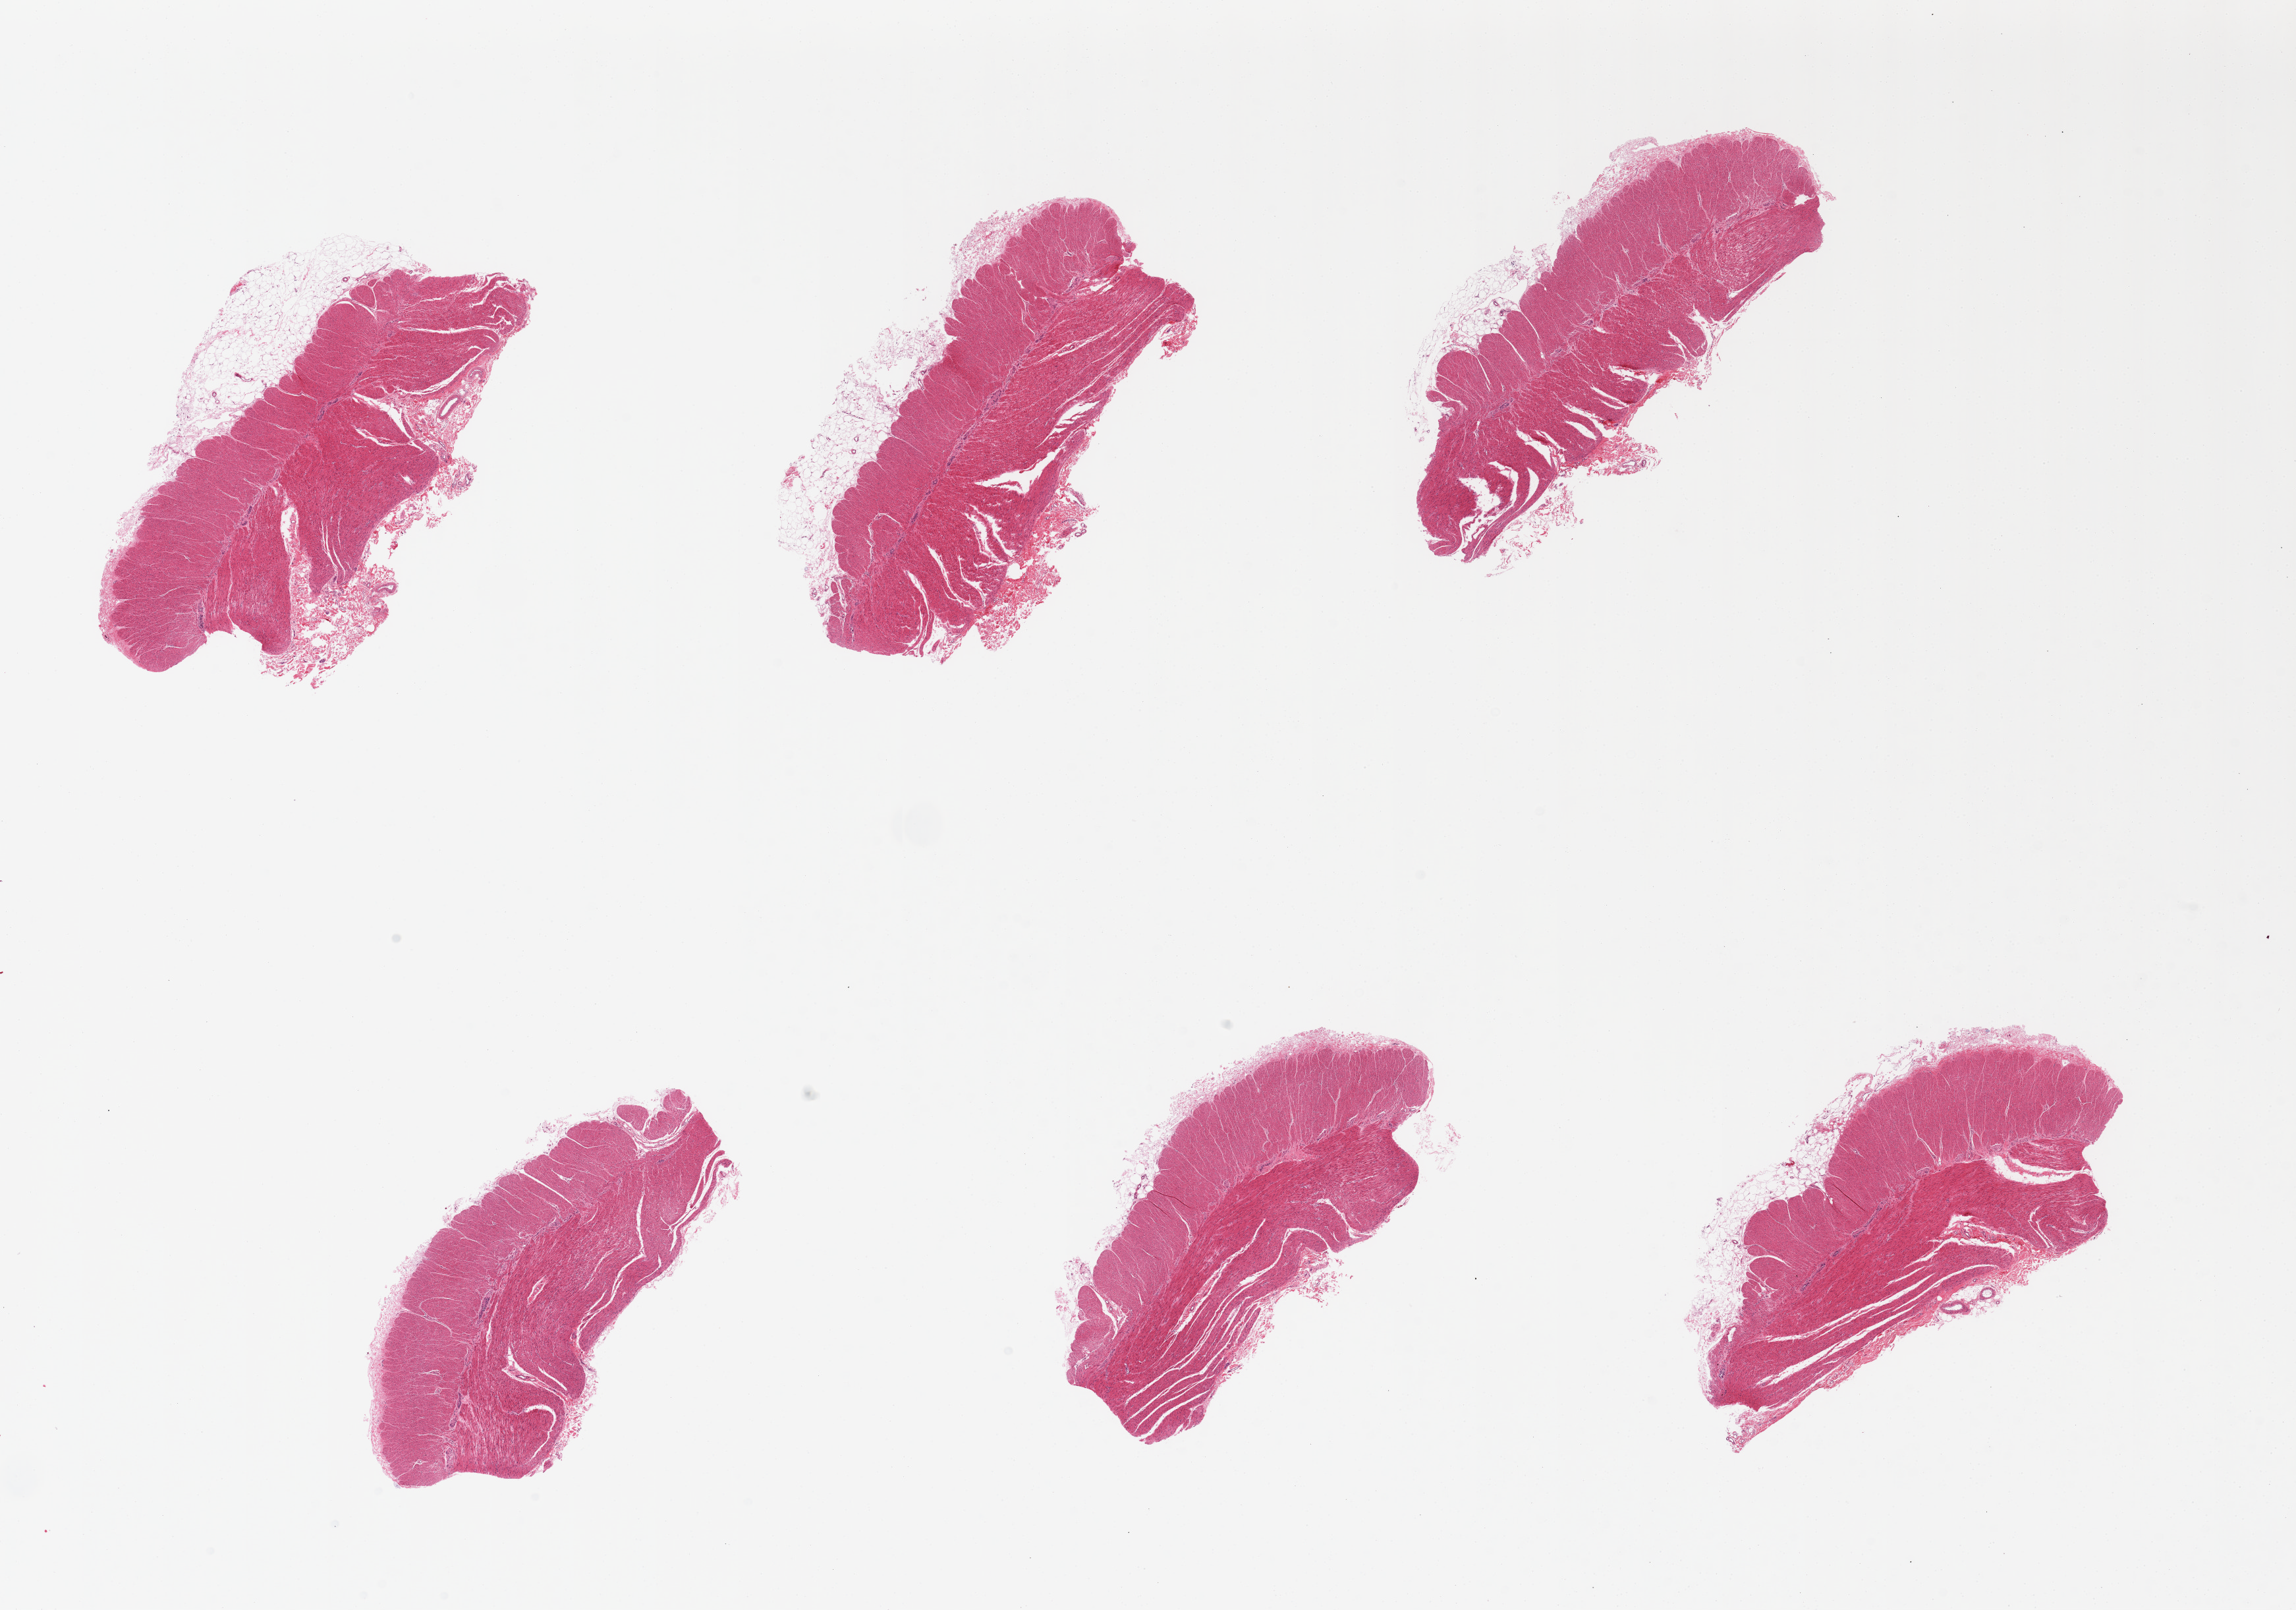
Whole-slide image, haematoxylin and eosin stain, a low-resolution overview of the entire scanned area, about 27.6 x 19.3 mm (slide scanned at 20x); PAXgene-fixed, paraffin-embedded tissue; sampled site (target tissue): sigmoid colon; donor tissue sample. Donor: male.
Pathologist's review note for this sample: 6 pieces; muscularis (target) with up to 1 mm external fat.